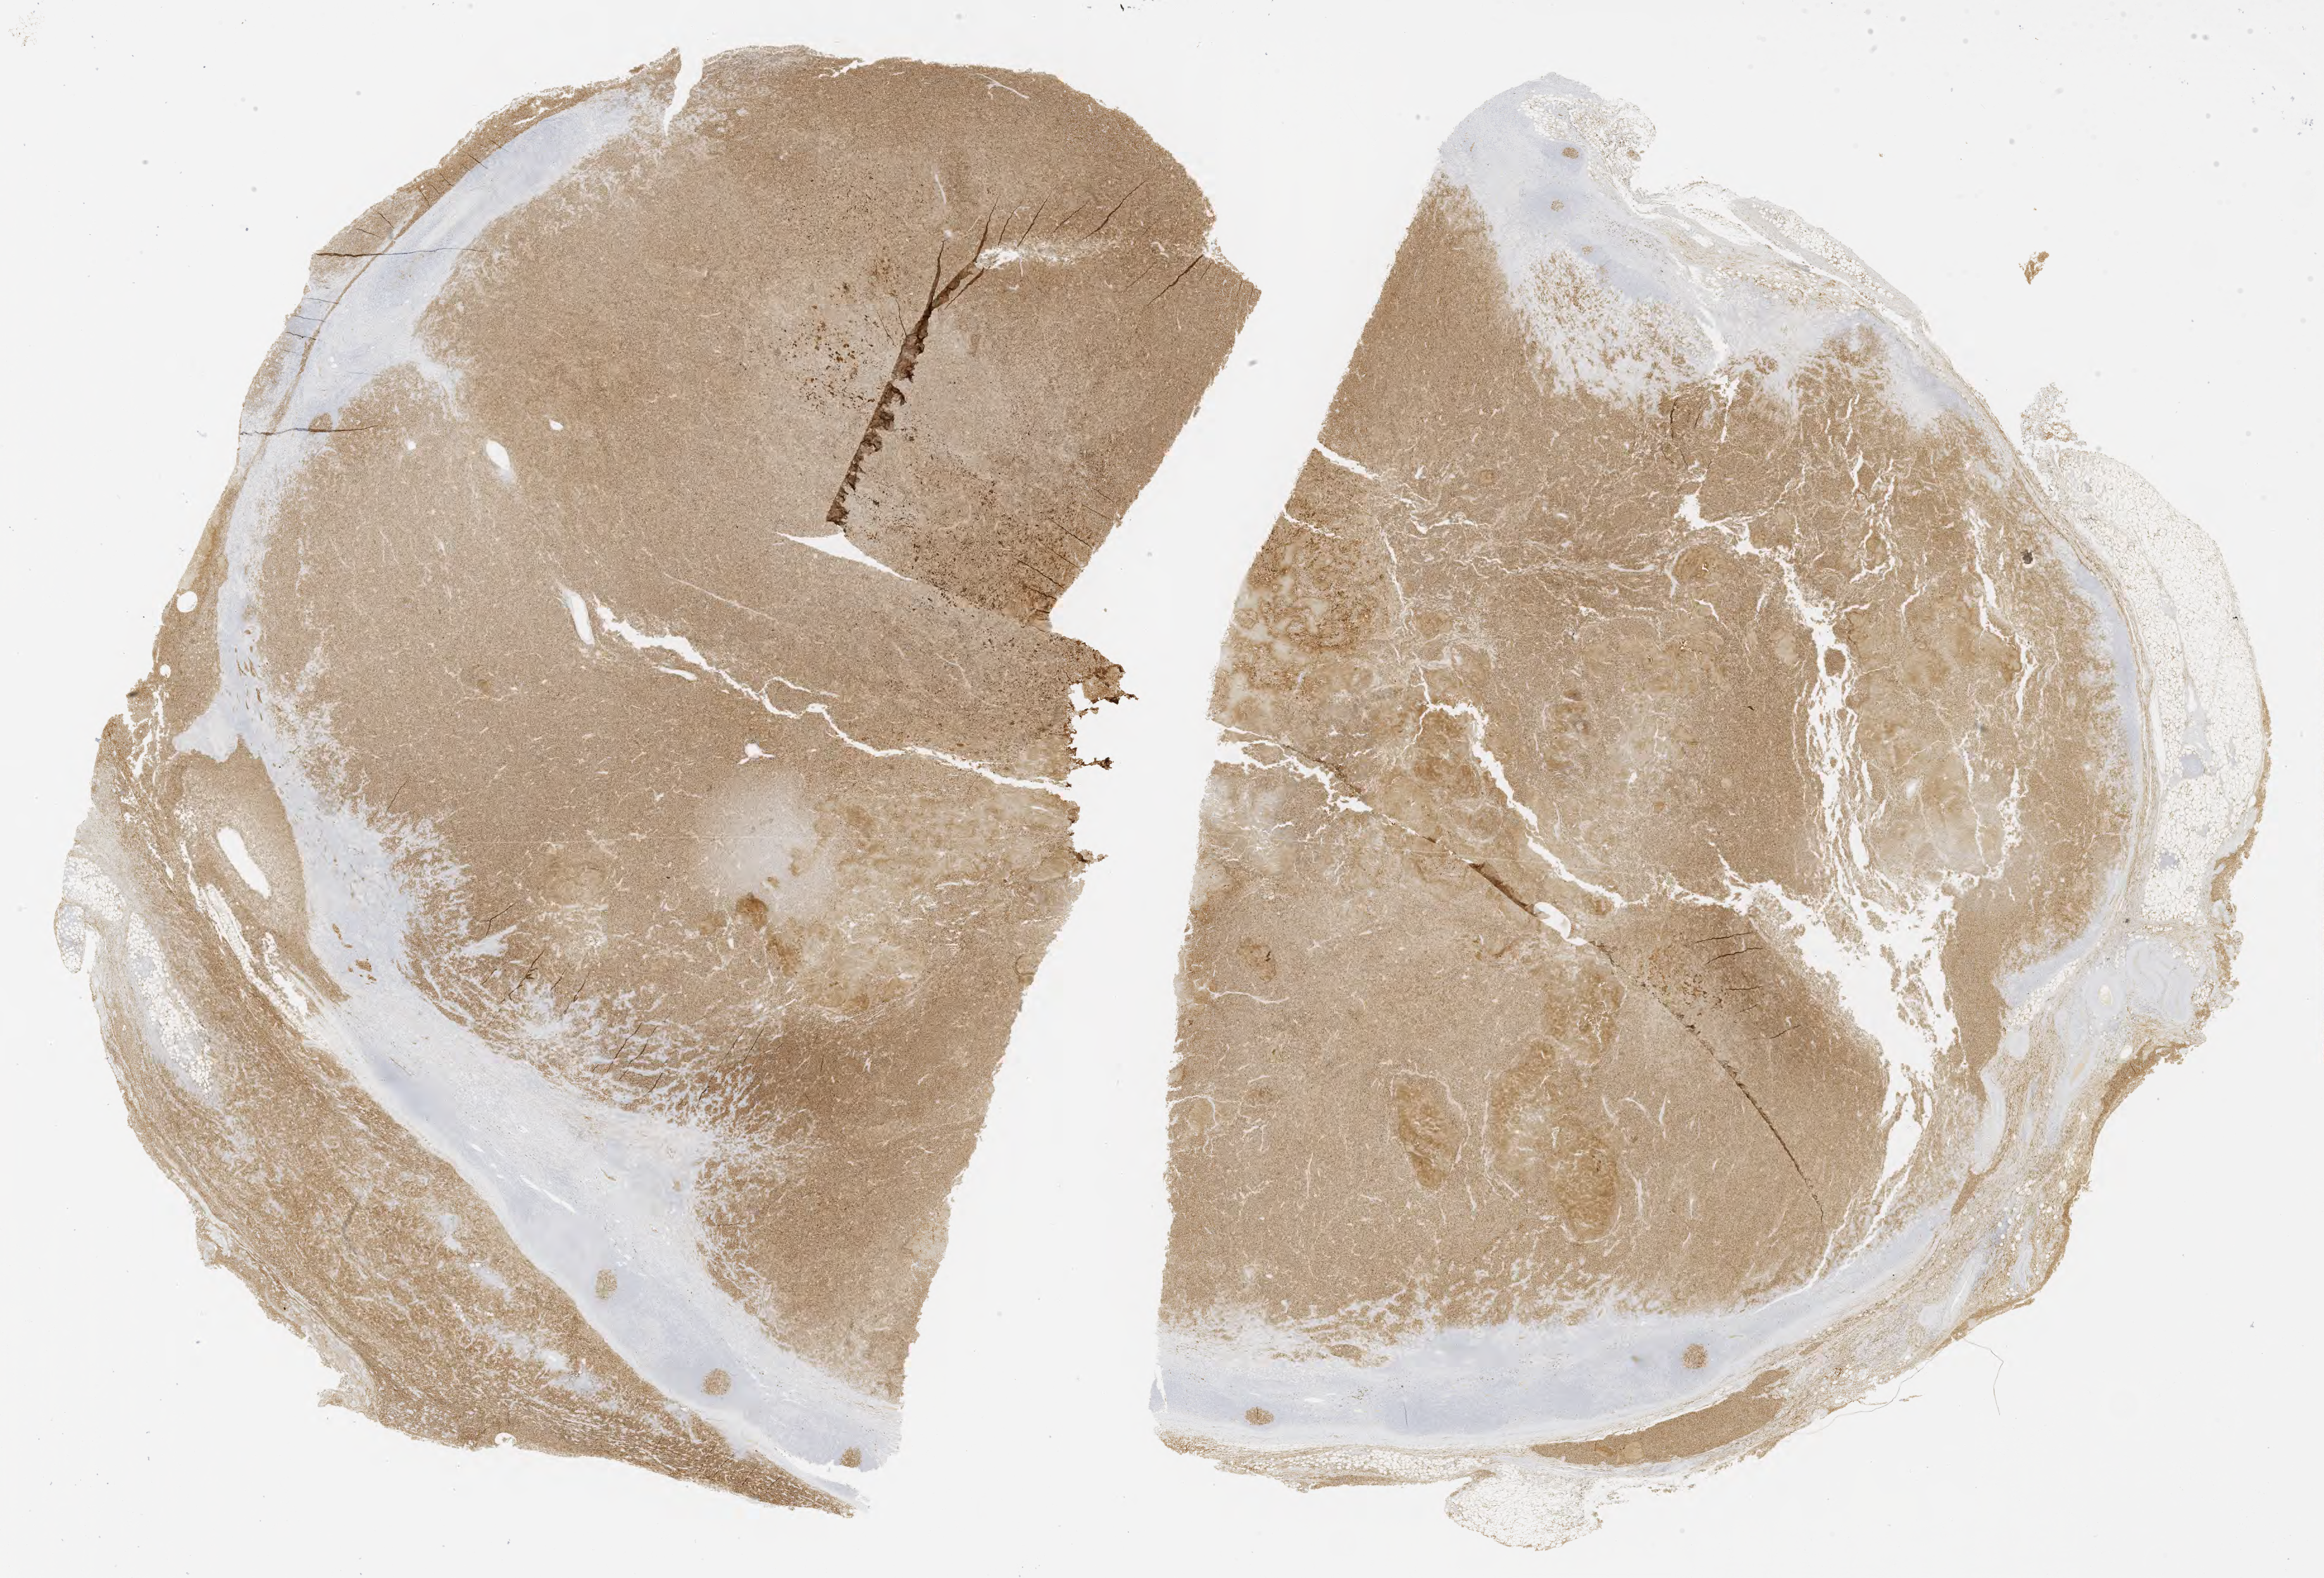
Whole-slide image, immunohistochemical stain for CD10, whole scanned area (about 29.7 x 20.2 mm) shown as a low-resolution overview; tumor tissue. Male patient, aged 48.
• diagnosis: Burkitt lymphoma, NOS